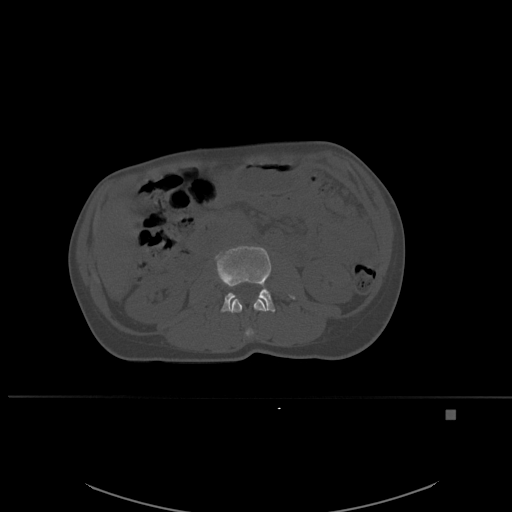
CT including the spine, one axial slice; slice 223 of 537 in the series (ordered by position); bone window (W 1800 / L 400 HU); 1.5 mm slice thickness; 512 × 512 image matrix, field of view 440 × 440 mm. Patient: female, 45 years. From the clinical record (not read from this slice): primary cancer: lung.
Structures marked on this image (semi-automatically segmented with operator editing):
- L2 vertebra: bounding box <230,298,267,337> (left, top, right, bottom; pixels)
- L3 vertebra: <215,244,295,312>